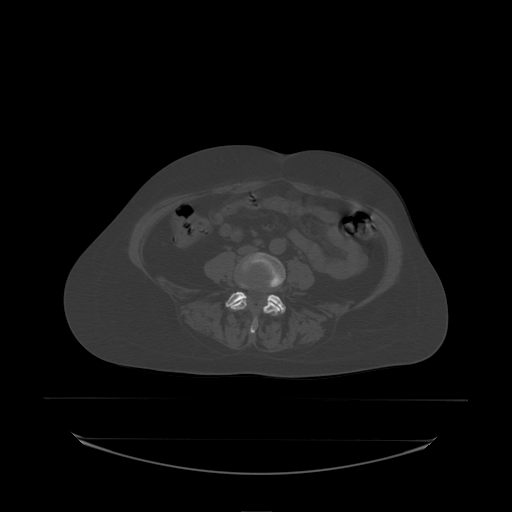
CT including the spine, one axial slice; slice 45 of 242 in the series (ordered by position); bone window (W 1800 / L 400 HU); 2.5 mm slice thickness; 512 × 512 image matrix, field of view 500 × 500 mm. Female patient, age 53 years. Case-level facts recorded for this patient, not image findings: primary cancer: lung.
Structures marked on this image (semi-automatically segmented with operator editing):
- L4 vertebra: bounding box (x1, y1, x2, y2) in pixels: (229, 252, 286, 334)
- L5 vertebra: (226, 265, 286, 314)